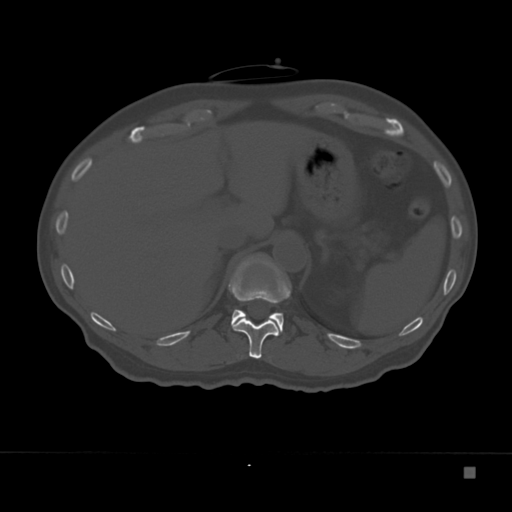
CT including the spine, one axial slice. Slice 145 of 332 in the series (ordered by position). Reconstruction kernel Br40s. Bone window (W 1800 / L 400 HU). 1.5 mm slice thickness. 512 × 512 image matrix. Patient: male, 72 years. From the clinical record (not read from this slice): primary cancer: skeletal.
Structures marked on this image (semi-automatically segmented with operator editing):
- T11 vertebra: bounding box [x1, y1, x2, y2] px = [228, 254, 291, 359]
- T12 vertebra: [231, 293, 284, 333]